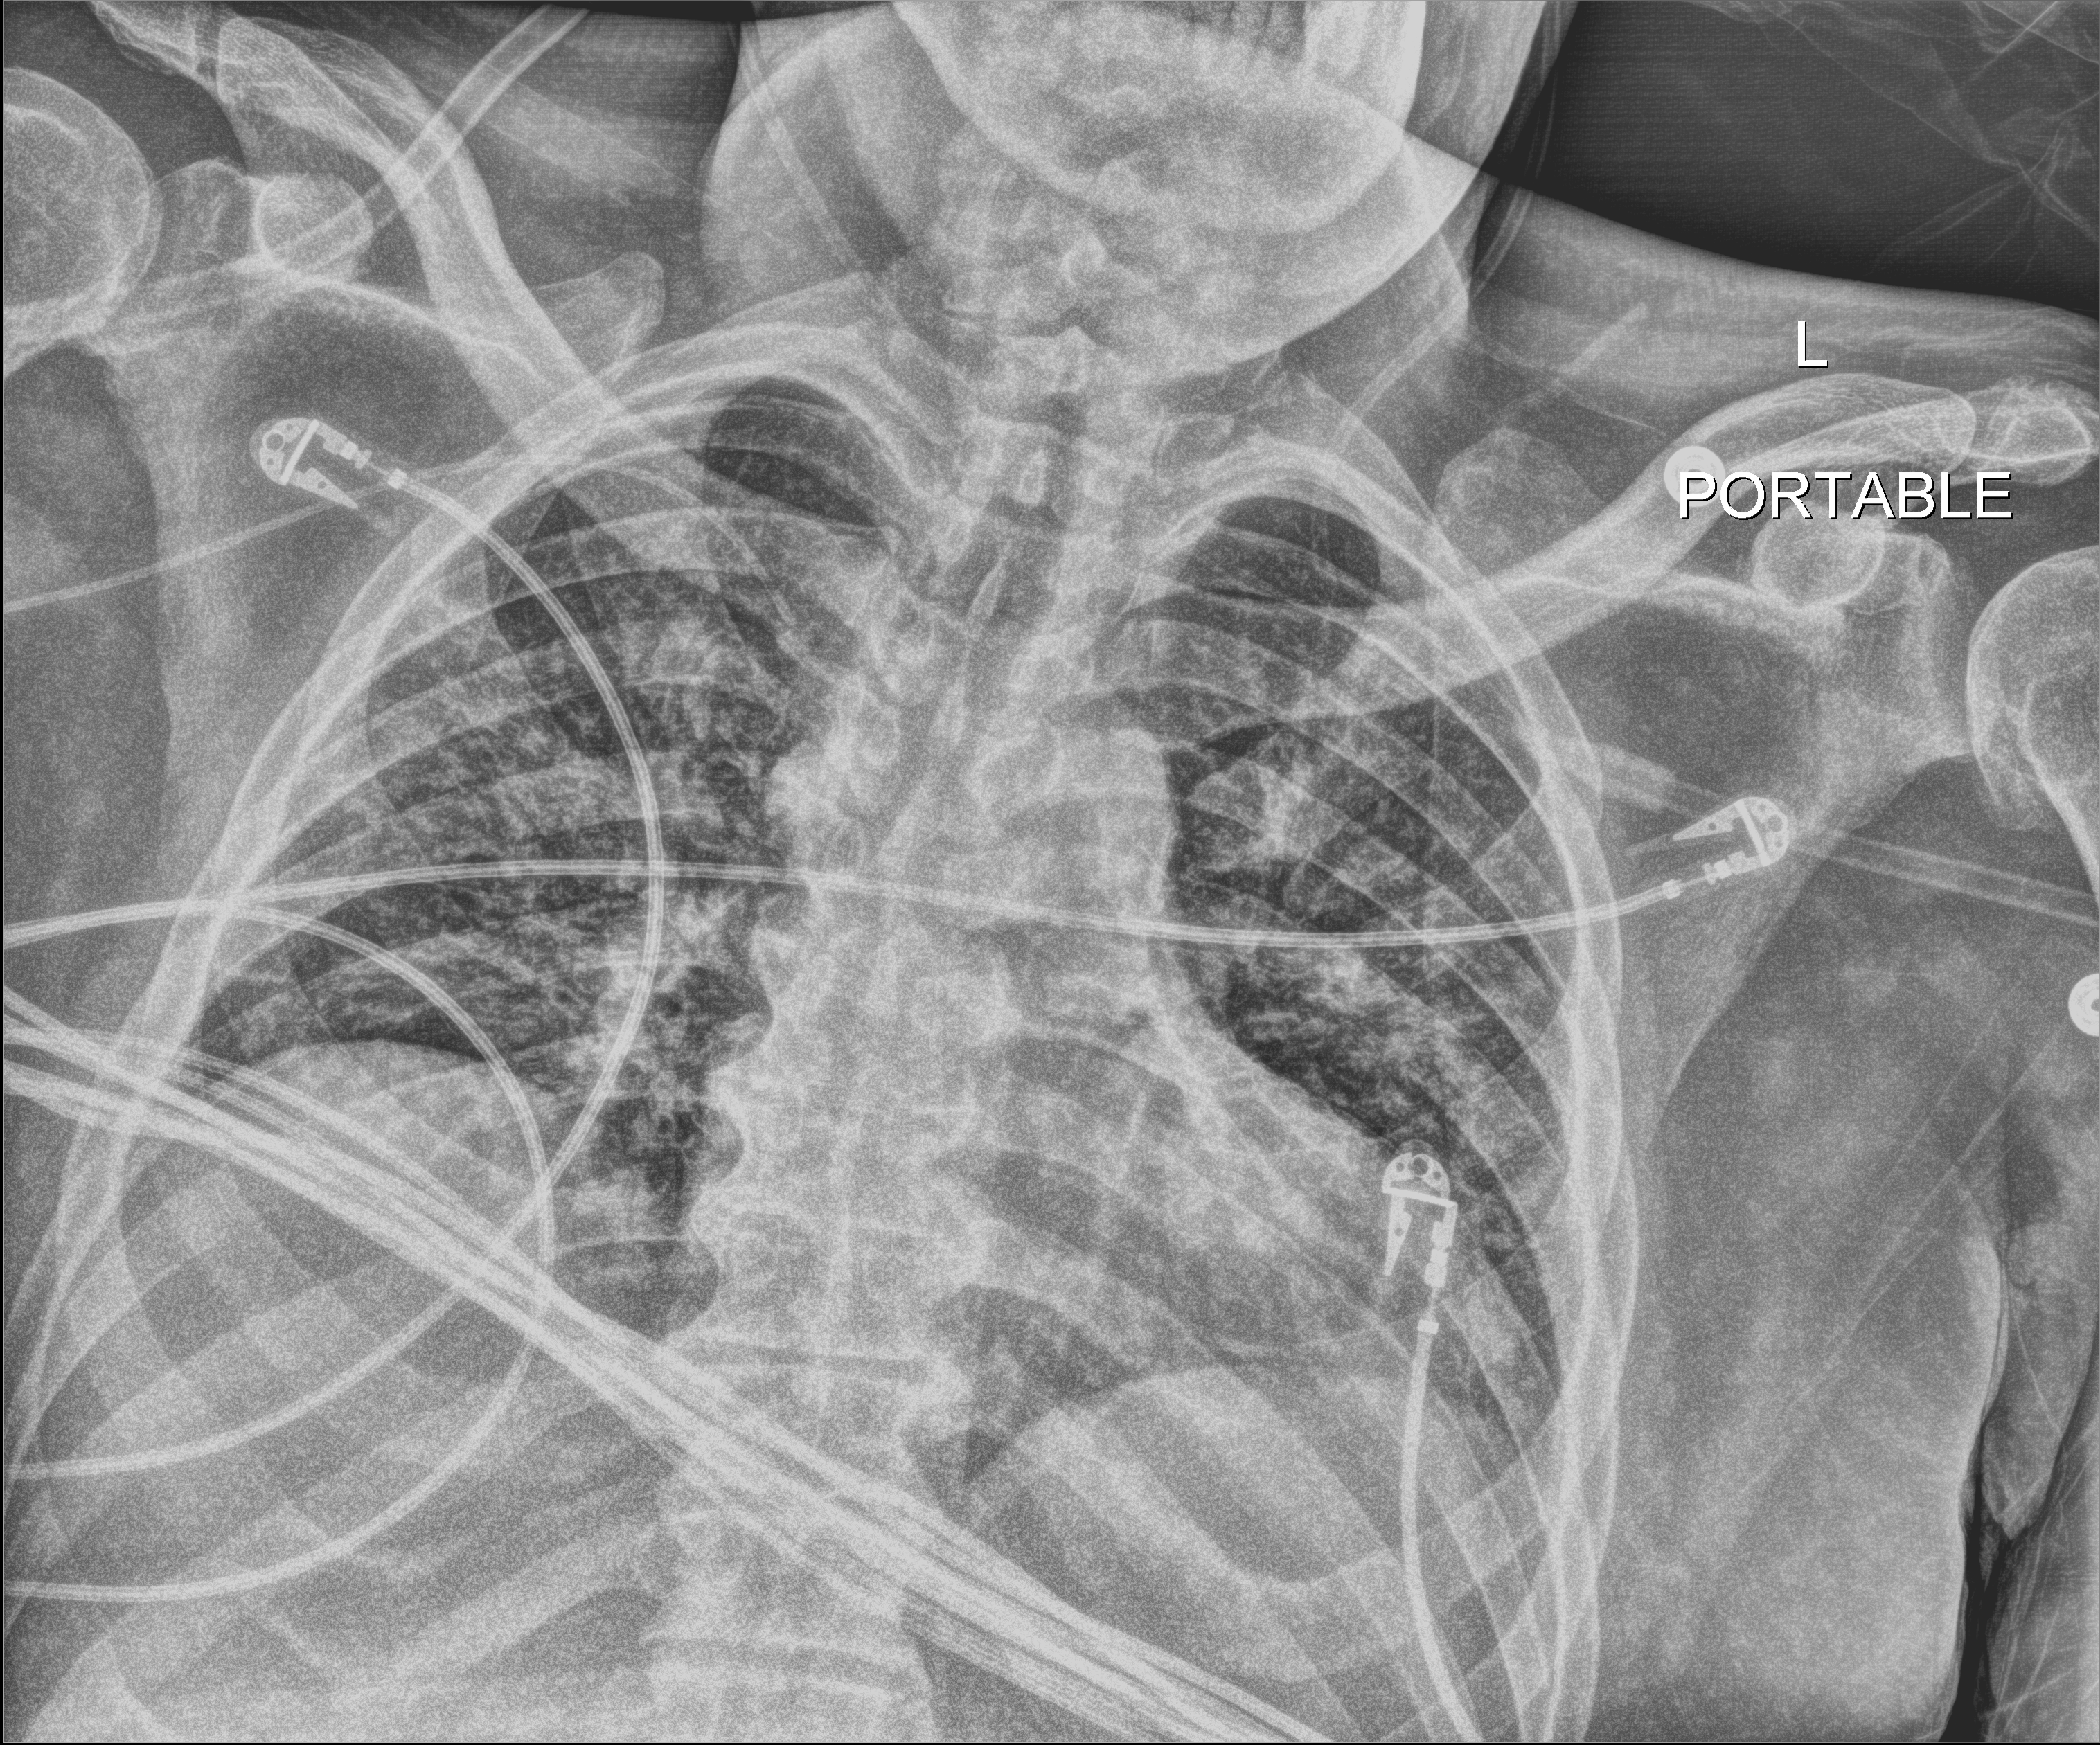
Portable chest radiograph, anteroposterior (AP) projection. Patient hospitalised with COVID-19; male, aged 18–59 years.
Admission-level facts for this patient (not findings on this image; timing relative to this image not recorded): length of hospital stay: 41 days; admitted to intensive care during this hospital stay: yes; COPD (admission record): no.